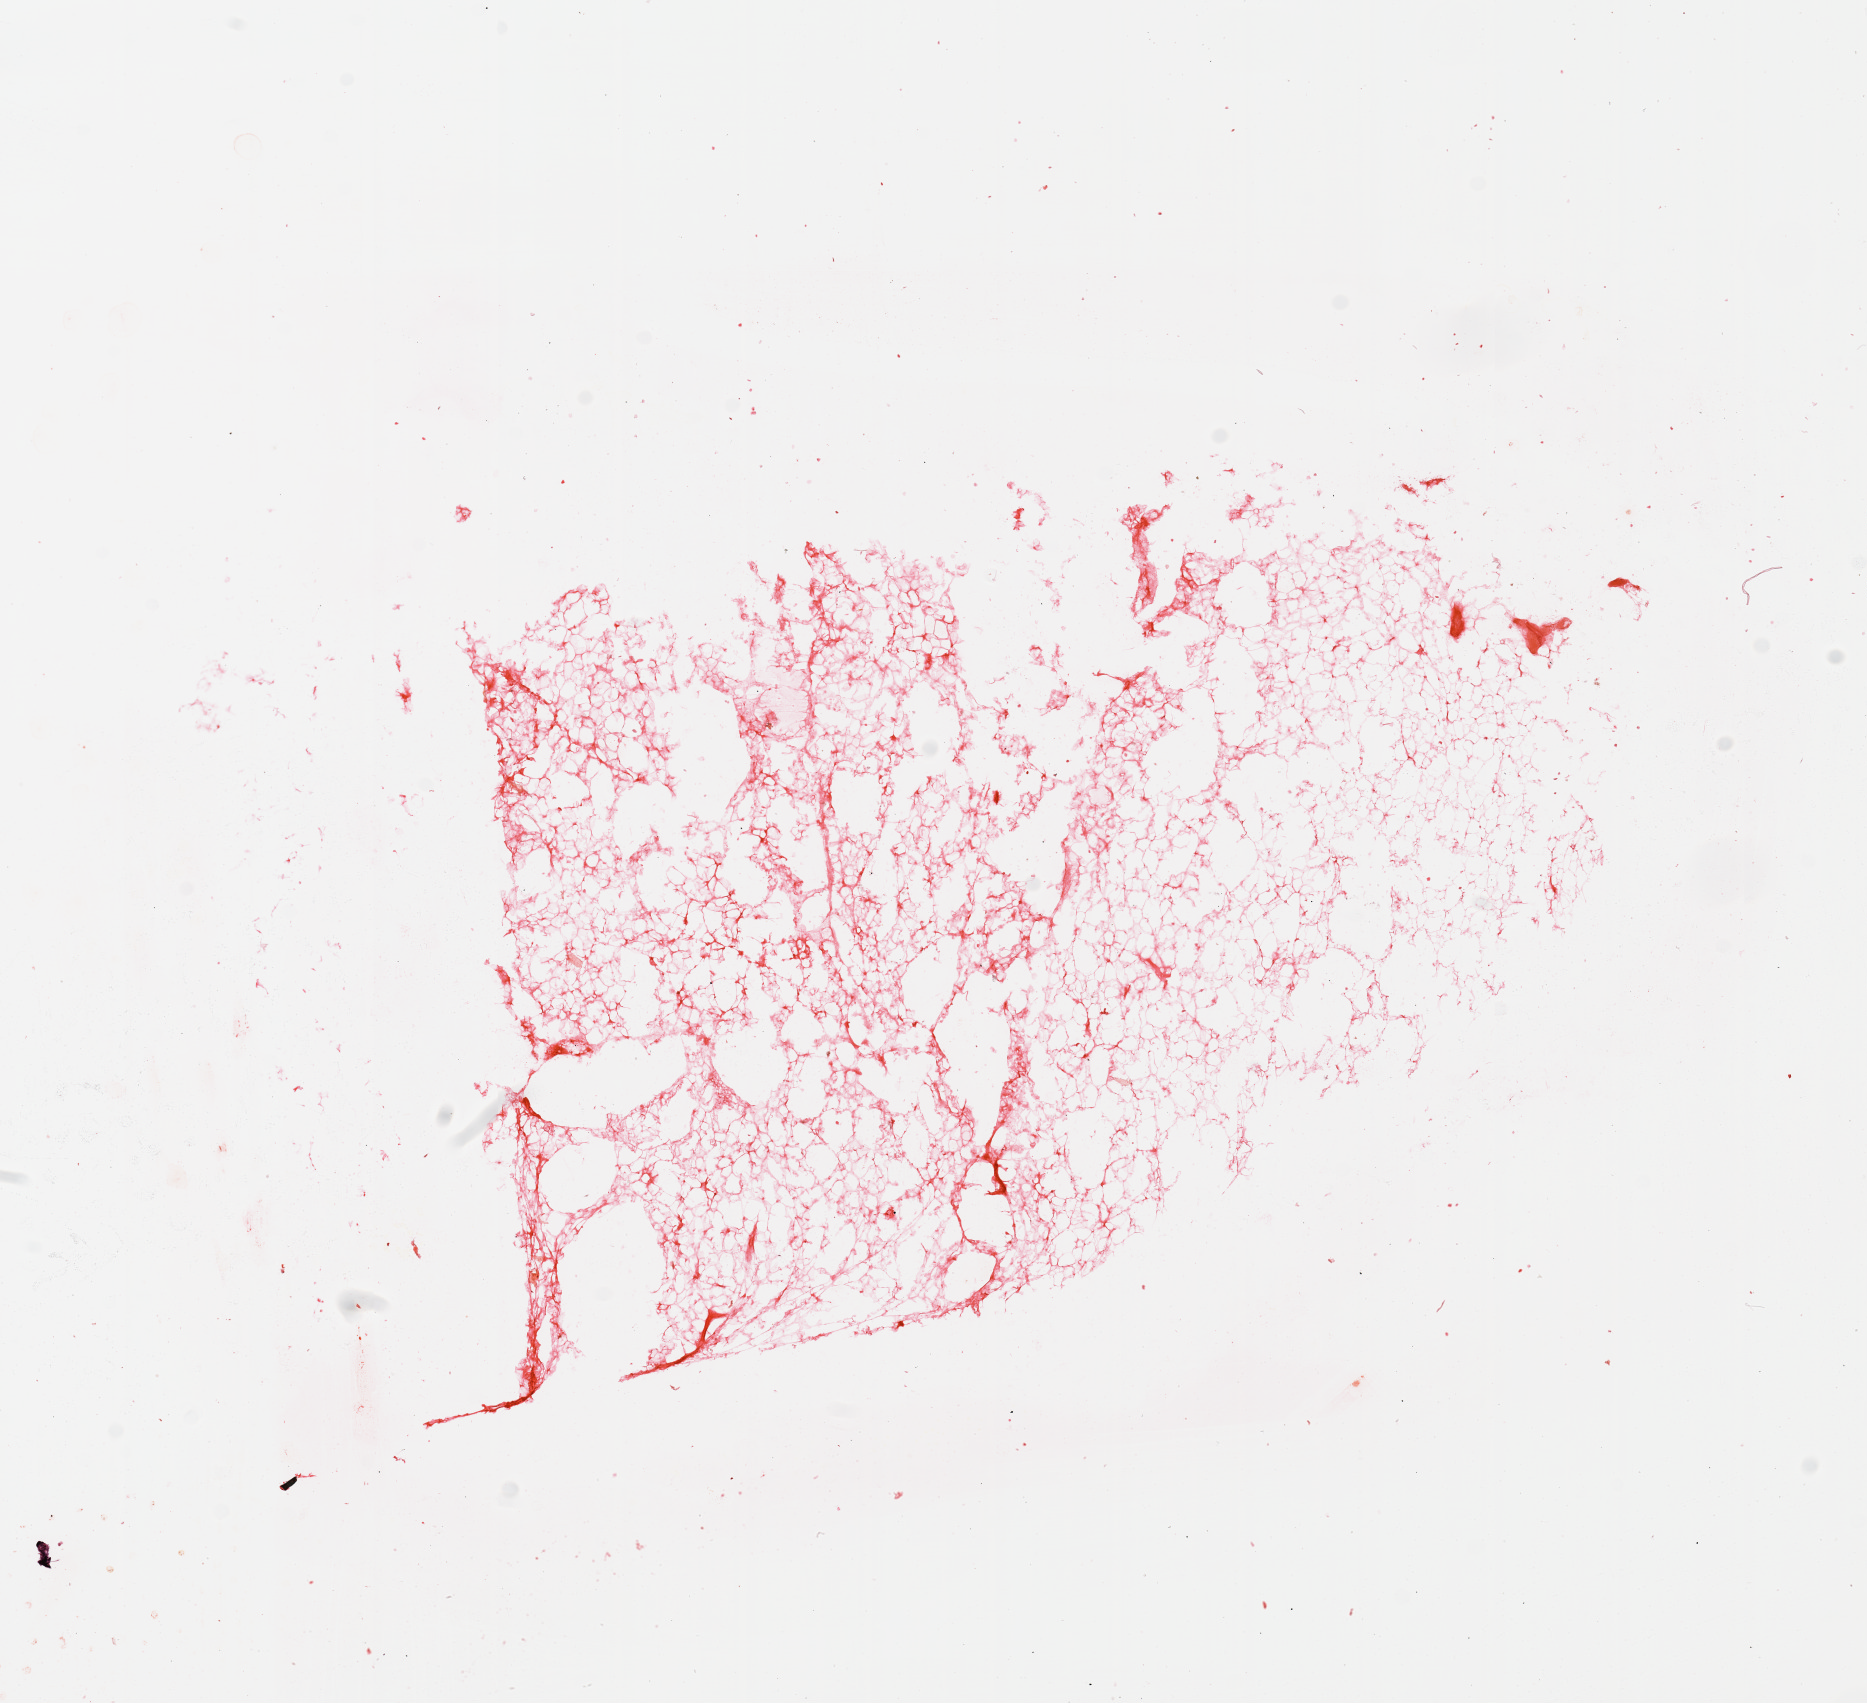
Digitized H&E tissue section (whole slide) — shown as a low-resolution overview of the whole scanned area (about 14.8 x 13.5 mm), normal (non-tumour) tissue sample, kidney. 57-year-old female patient.
This section: normal (non-tumour) tissue from the same patient. Patient diagnosis: Renal cell carcinoma, NOS.